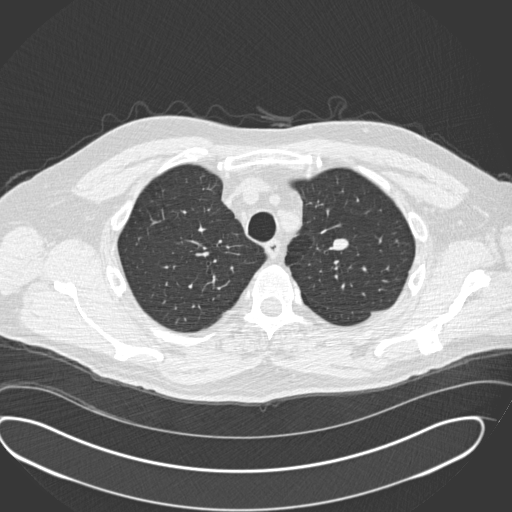
Axial slice from a low-dose chest CT screening exam. Second annual screen. Lung window (W 1500 / L -600 HU). Standard (soft-tissue) reconstruction kernel (B30f). Slice 44 of 190 in the series. Male participant, aged 56 years at enrolment. Current smoker at enrolment.
- Lesion marked by an expert reader, bounding box (x1, y1, x2, y2) in pixels: (312, 226, 368, 270).
- Screening reader's record for this exam: no non-calcified nodule ≥4 mm recorded.
- Later outcome: lung cancer diagnosed 520 days after this screen (after the third annual screen) — neuroendocrine carcinoma, NOS, left upper lobe, well differentiated (G1), stage IA (AJCC 6th edition), 20 mm at pathology.